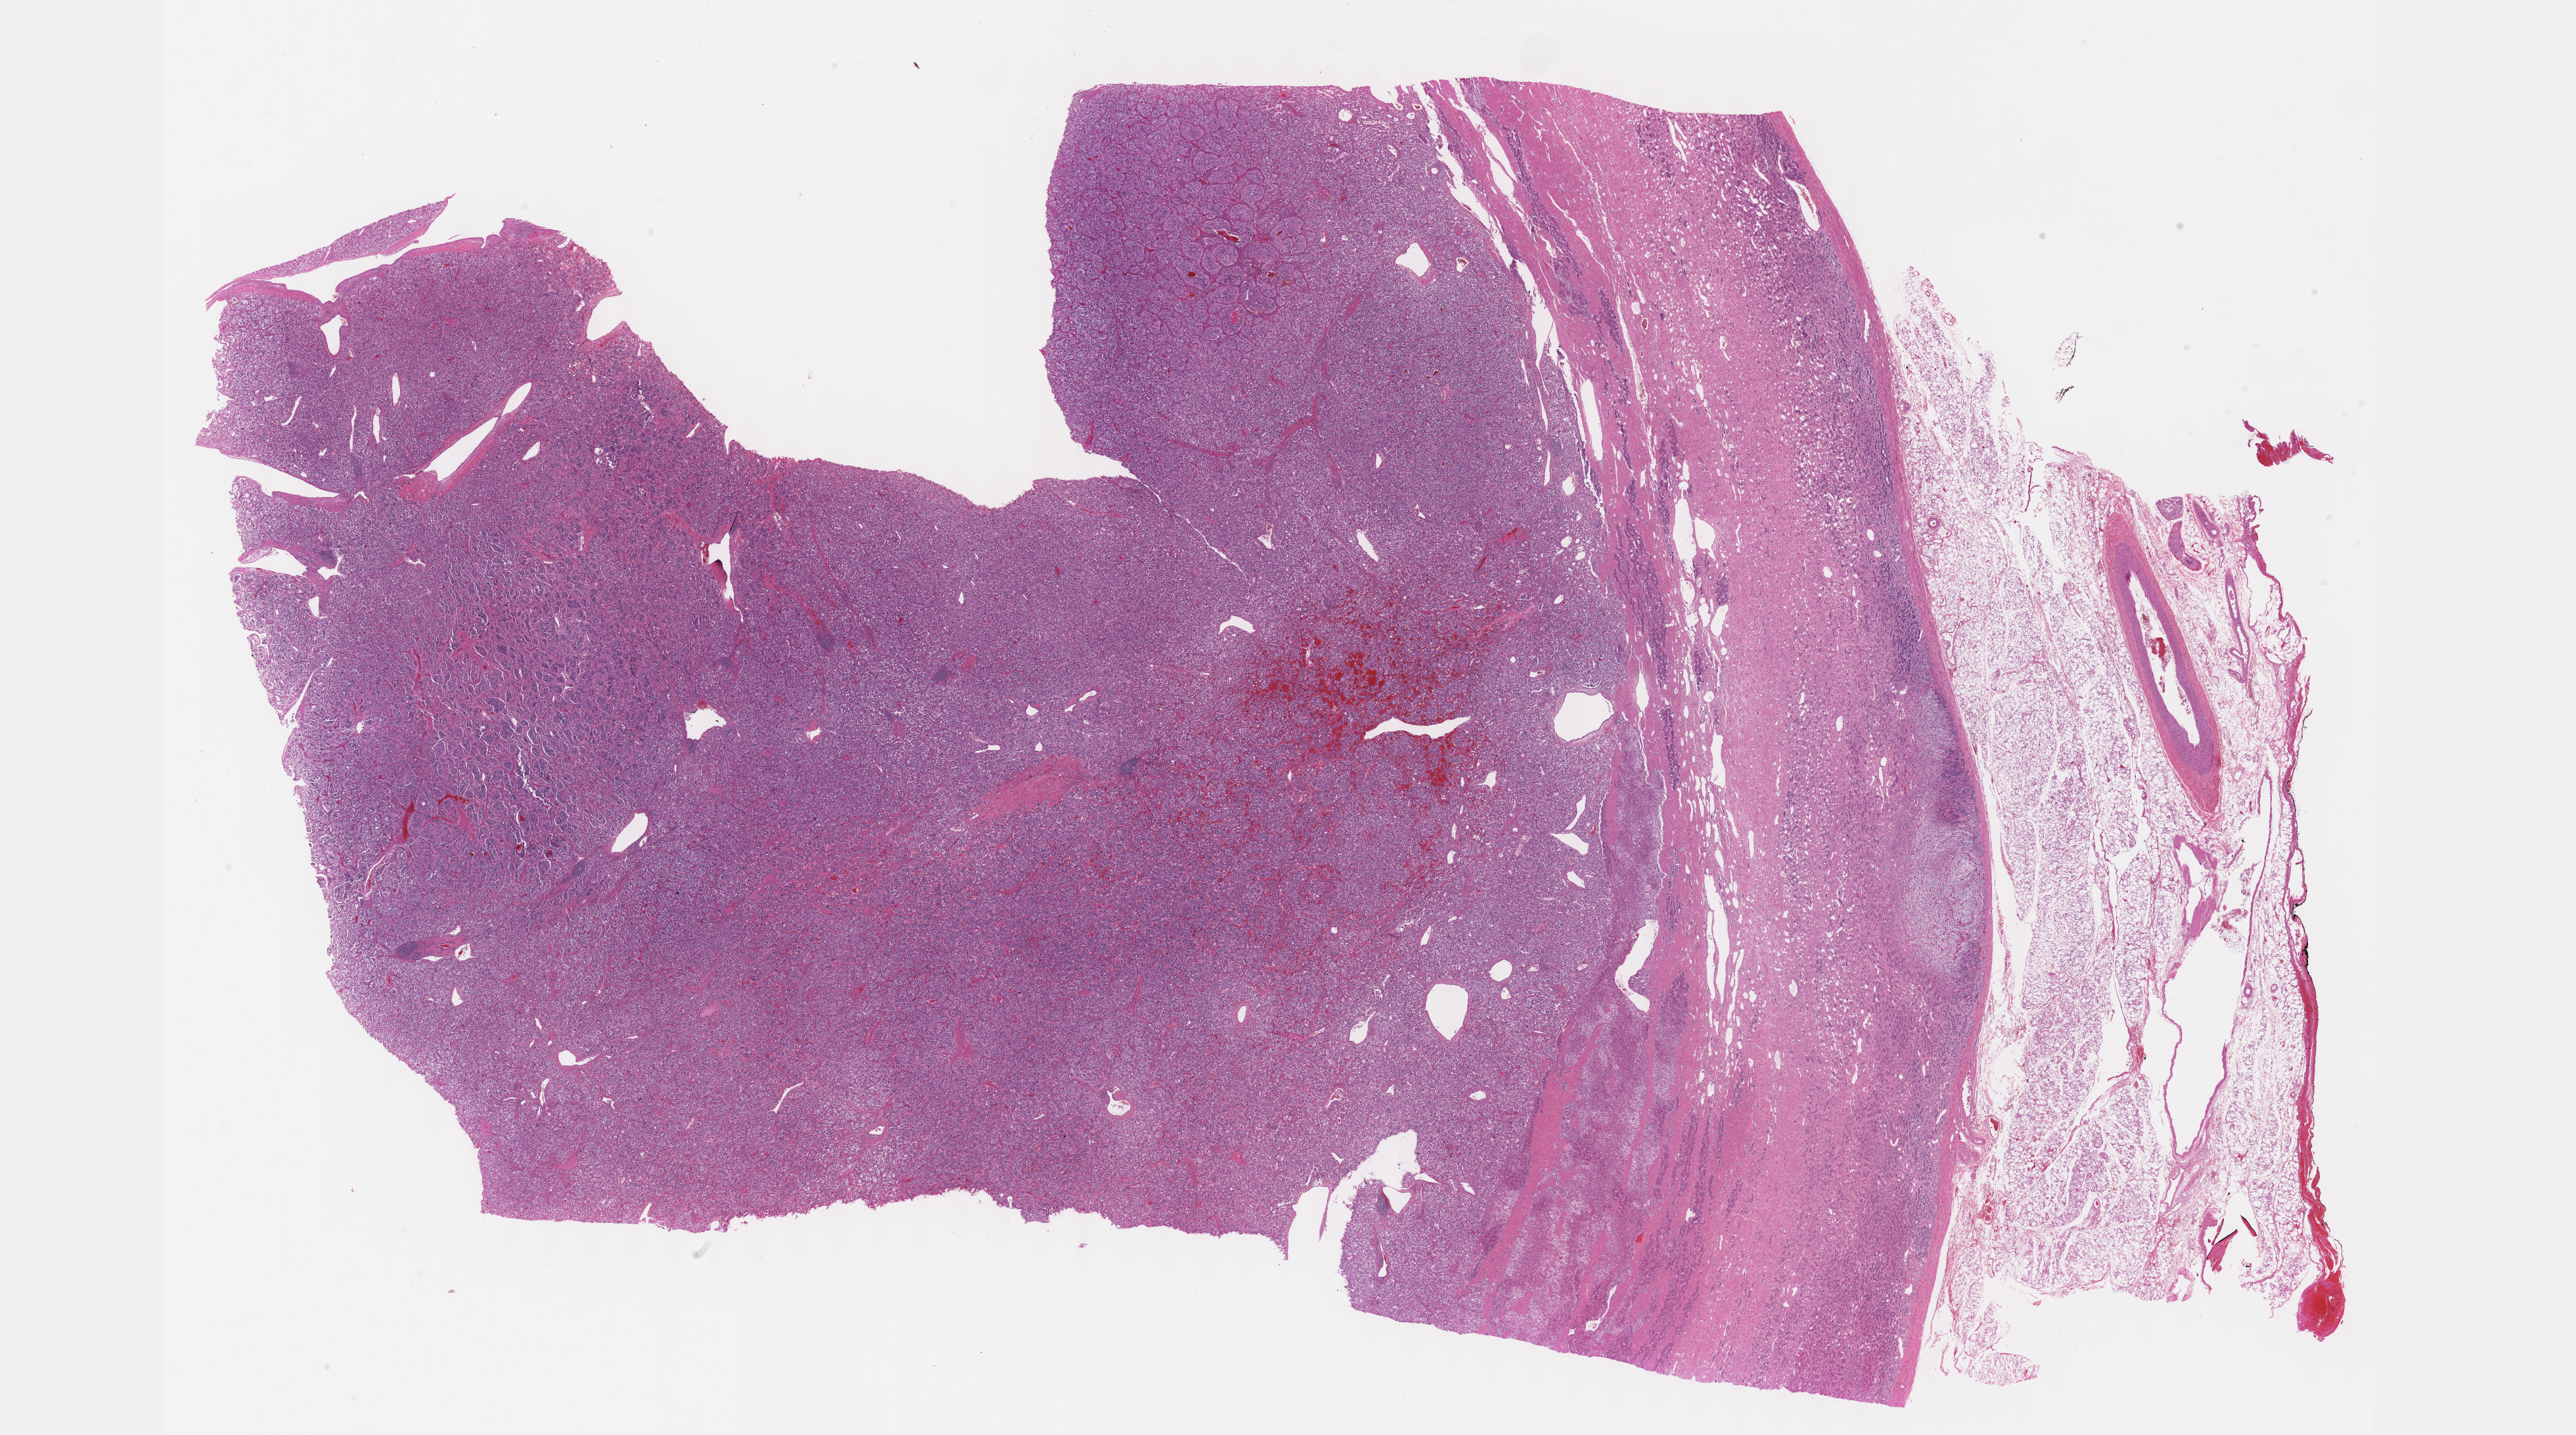
Whole-slide histology image, H&E-stained, shown as a low-resolution overview of the whole scanned area (about 31.7 x 17.7 mm, slide scanned at 40x), FFPE section, adrenal gland, primary tumour sample. Male patient; age at initial diagnosis 32 years.
Pathologic diagnosis: Pheochromocytoma, NOS.